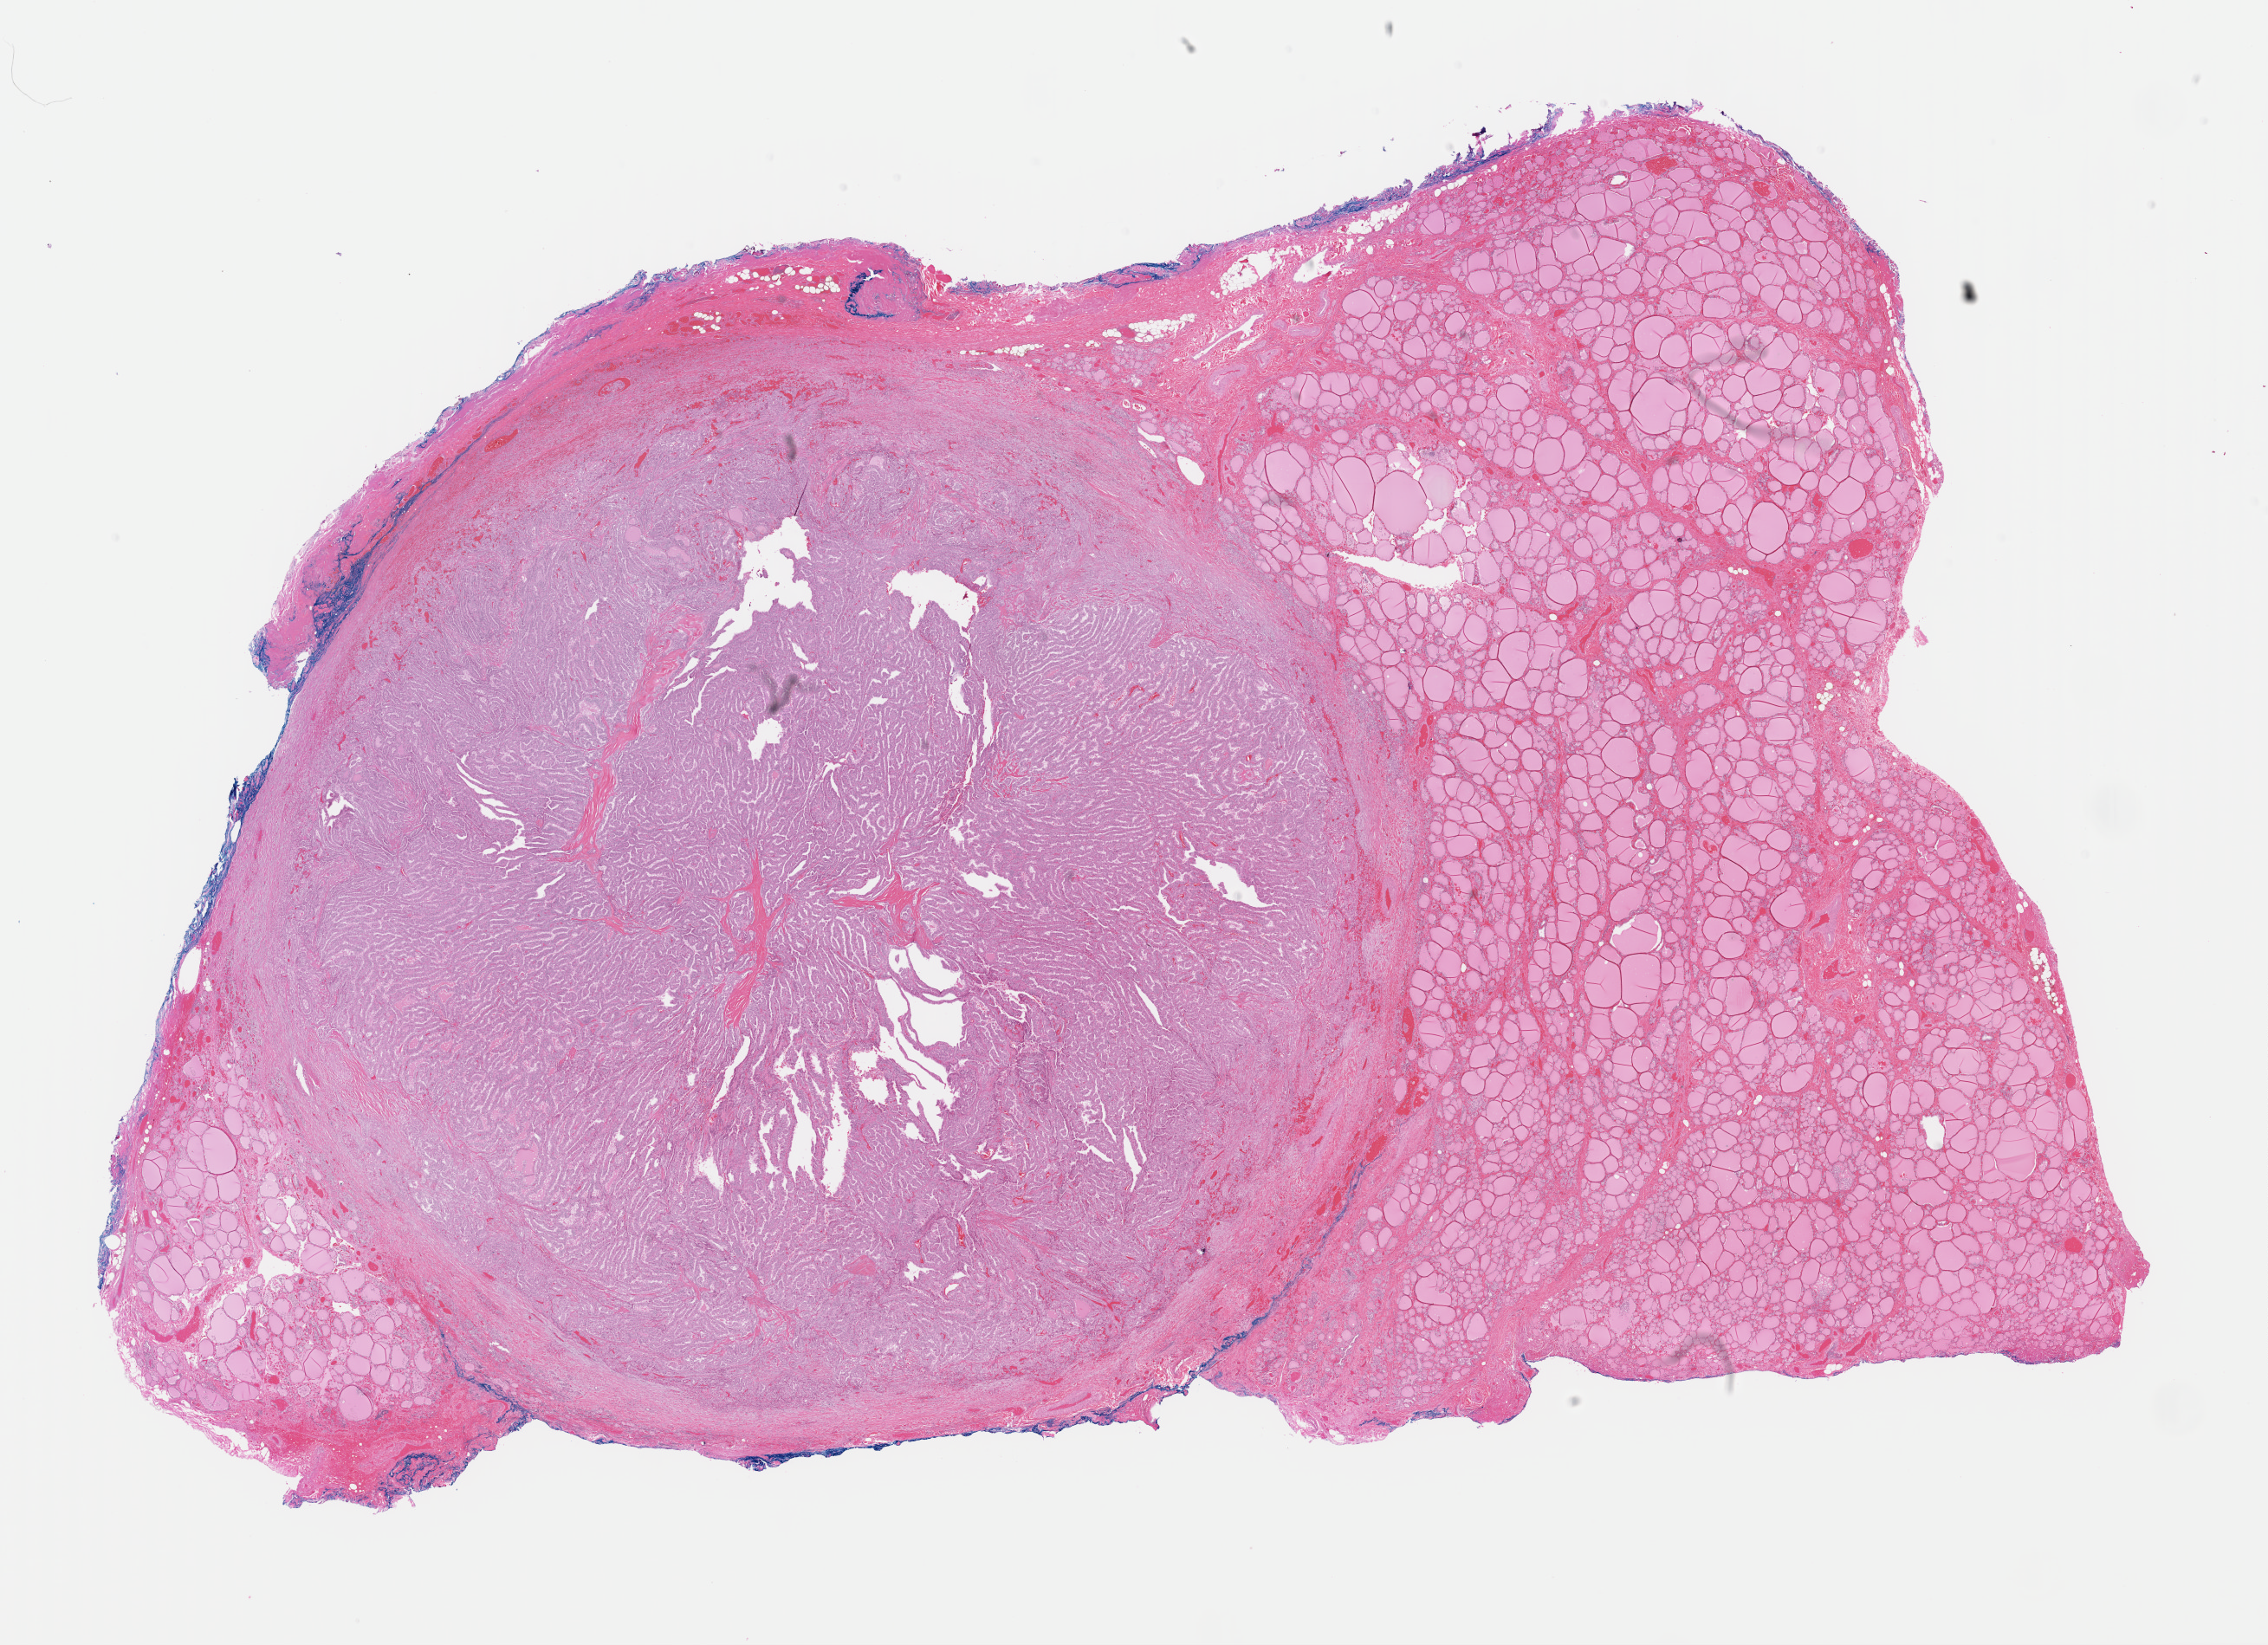
Whole-slide histology image, H&E-stained, low-resolution overview of the scanned area, about 20.7 x 15.0 mm. FFPE section. Primary tumour sample from the thyroid. Female, age 34 years at initial diagnosis.
* AJCC pathologic stage: I (6th edition)
* diagnosis: Papillary adenocarcinoma, NOS (thyroid gland)
* lymph nodes positive (case pathology): 7 of 25 examined